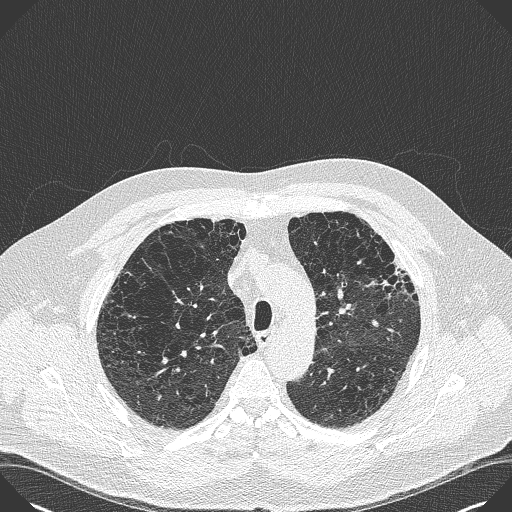
Low-dose screening chest CT, axial slice; baseline annual screen; lung window (W 1500 / L -600 HU); 1 mm slice thickness; 120 kVp; slice 108 of 383 in the series. Male, age 59 years at enrolment.
Lesion marked by an expert reader, bounding box [x1, y1, x2, y2] px = [372, 252, 430, 304]. Screening reader's record for this exam: no non-calcified nodule ≥4 mm recorded. Official screen result: negative screen, minor abnormalities not suspicious for lung cancer. Lung cancer was diagnosed 909 days after this screen: bronchiolo-alveolar carcinoma, mixed mucinous and non-mucinous, left upper lobe, stage IA (AJCC 6th edition), 20 mm at pathology.